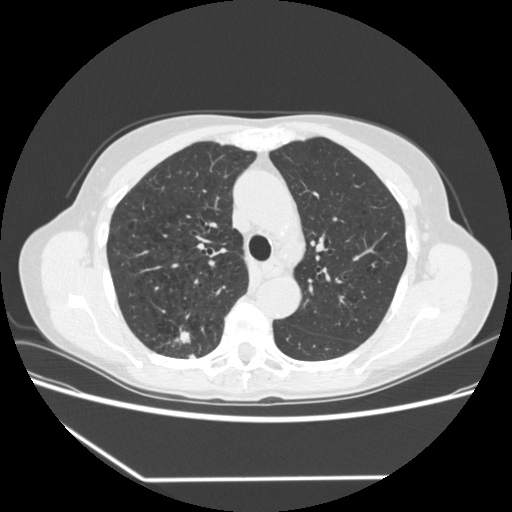
Low-dose screening chest CT, one axial slice; position 235 of 323 along the scan axis; 120 kVp; lung window (W 1500 / L -600 HU); 1.25 mm slice thickness; 512 × 512 image matrix, field of view 360 × 360 mm.
Annotated regions visible in this slice (manually delineated by an expert):
- lesion 1 (tumor, upper lobe of right lung): box from (x=174, y=327) to (x=191, y=344) px